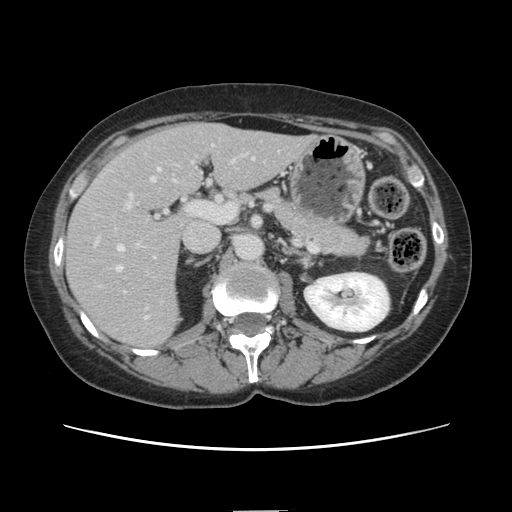
Contrast-enhanced abdominal CT, one axial slice; position 72 of 141 along the scan axis; 120 kVp; soft-tissue window (W 400 / L 40 HU); 2.5 mm slice thickness; 512 × 512 image matrix, field of view 350 × 350 mm. Female patient, age 63 years. From the clinical record (not read from this slice): diagnosis: colorectal cancer liver metastases, imaged before liver resection; multiple liver metastases: yes; largest metastasis: 3.2 cm; disease in both lobes: yes.
Annotated regions visible in this slice (expert manual segmentation):
- hepatic veins: bounding box <115,169,160,272> (left, top, right, bottom; pixels)
- liver: <68,125,308,348>
- planned liver remnant (the part of the liver to remain after resection): <175,124,309,192>
- portal vein (with intrahepatic branches): <125,192,148,318>